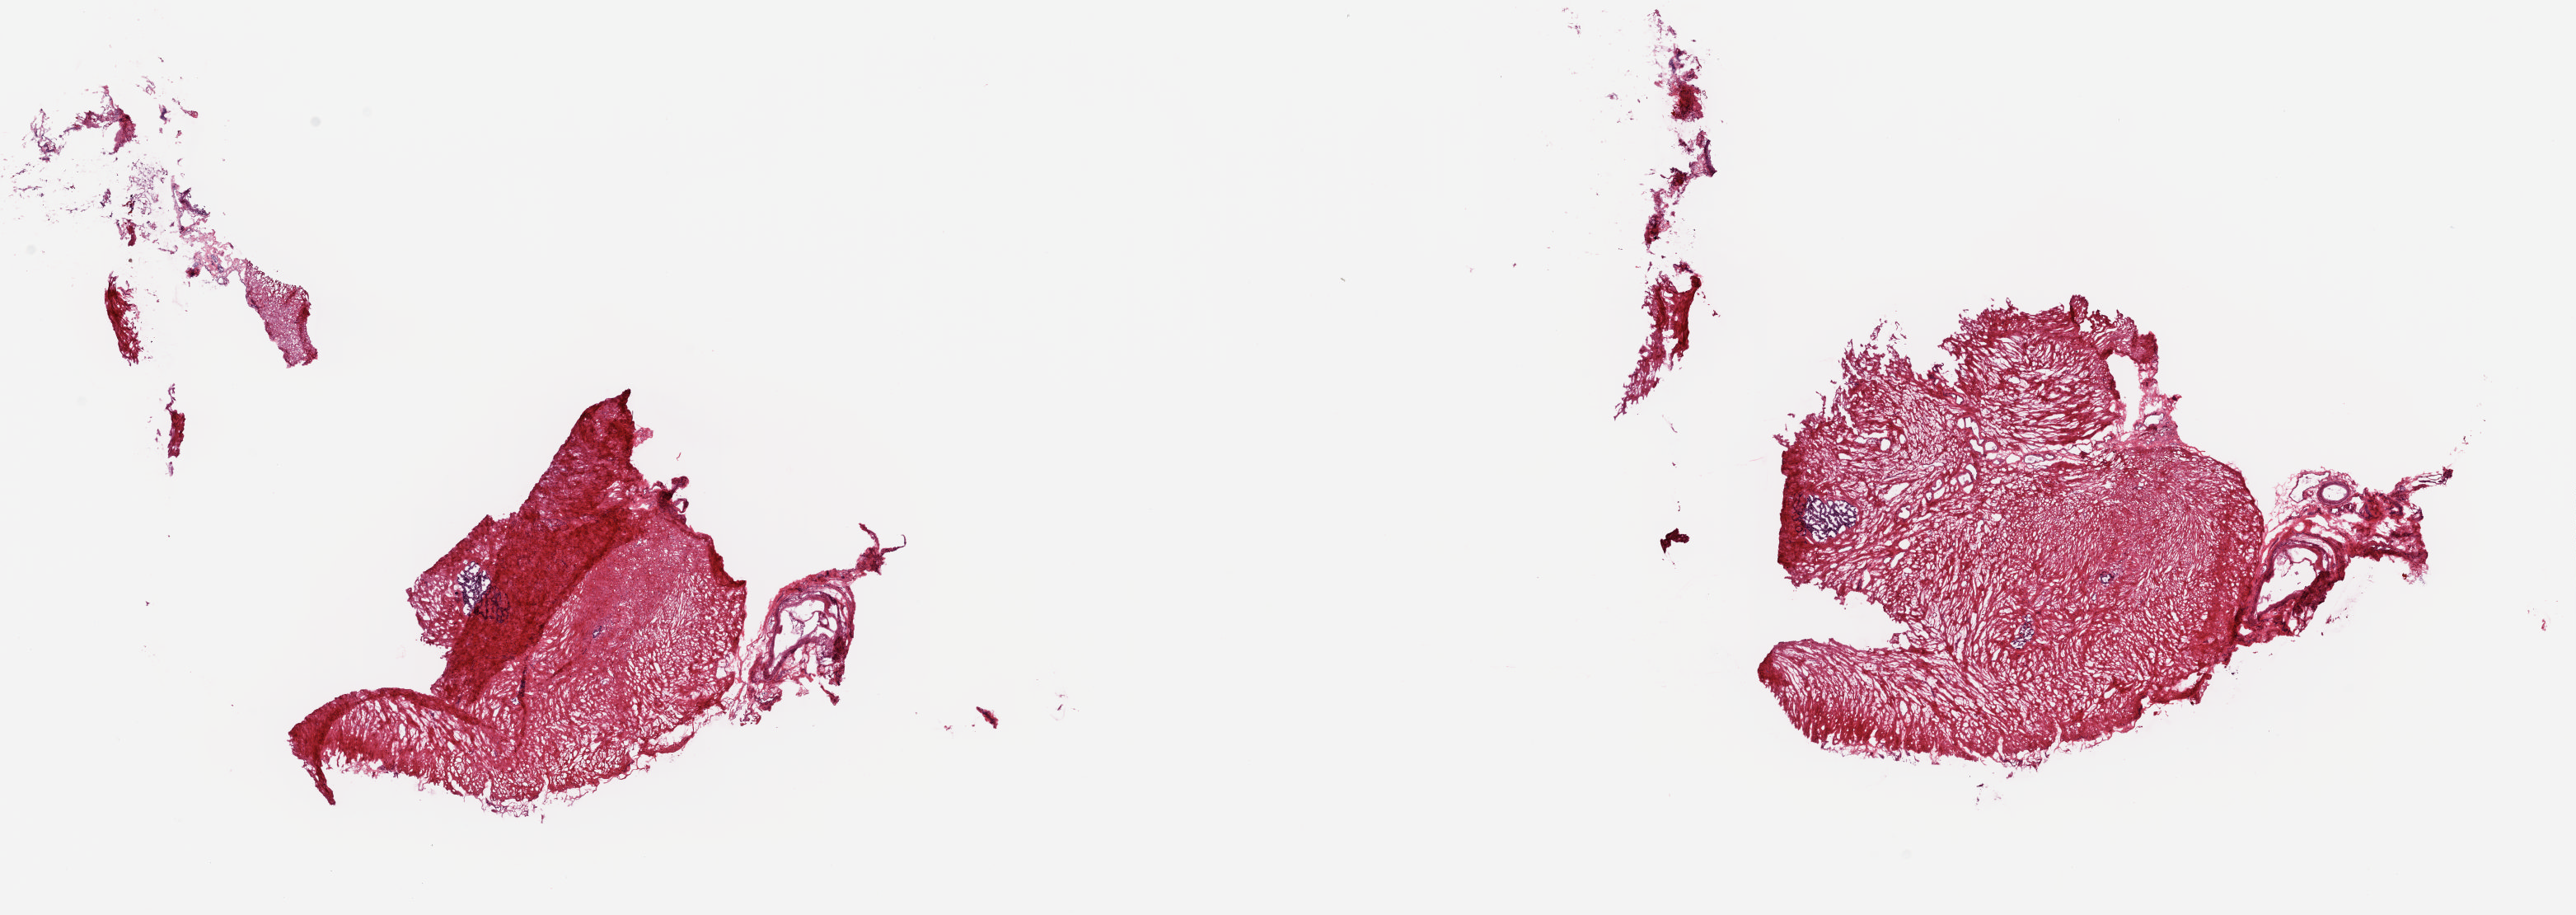
Whole-slide histology image, Hematoxylin and eosin (H&E) stained — shown as a low-resolution overview of the whole scanned area (about 24.8 x 8.8 mm, slide scanned at 20x). Frozen section. Sample: solid tissue normal (non-tumour tissue), prostate. Male, age 58 years at initial diagnosis. Slide review estimates, as recorded: tumour cells 0%, tumour nuclei 0%, normal cells 100%, stromal cells 0%, necrosis 0%. Infiltration values recorded for this section: lymphocyte infiltration 0%, monocyte infiltration 0%, neutrophil infiltration 0%.
- this section: solid tissue normal sample (biorepository sample class)
- patient diagnosis: Adenocarcinoma, NOS (prostate gland)